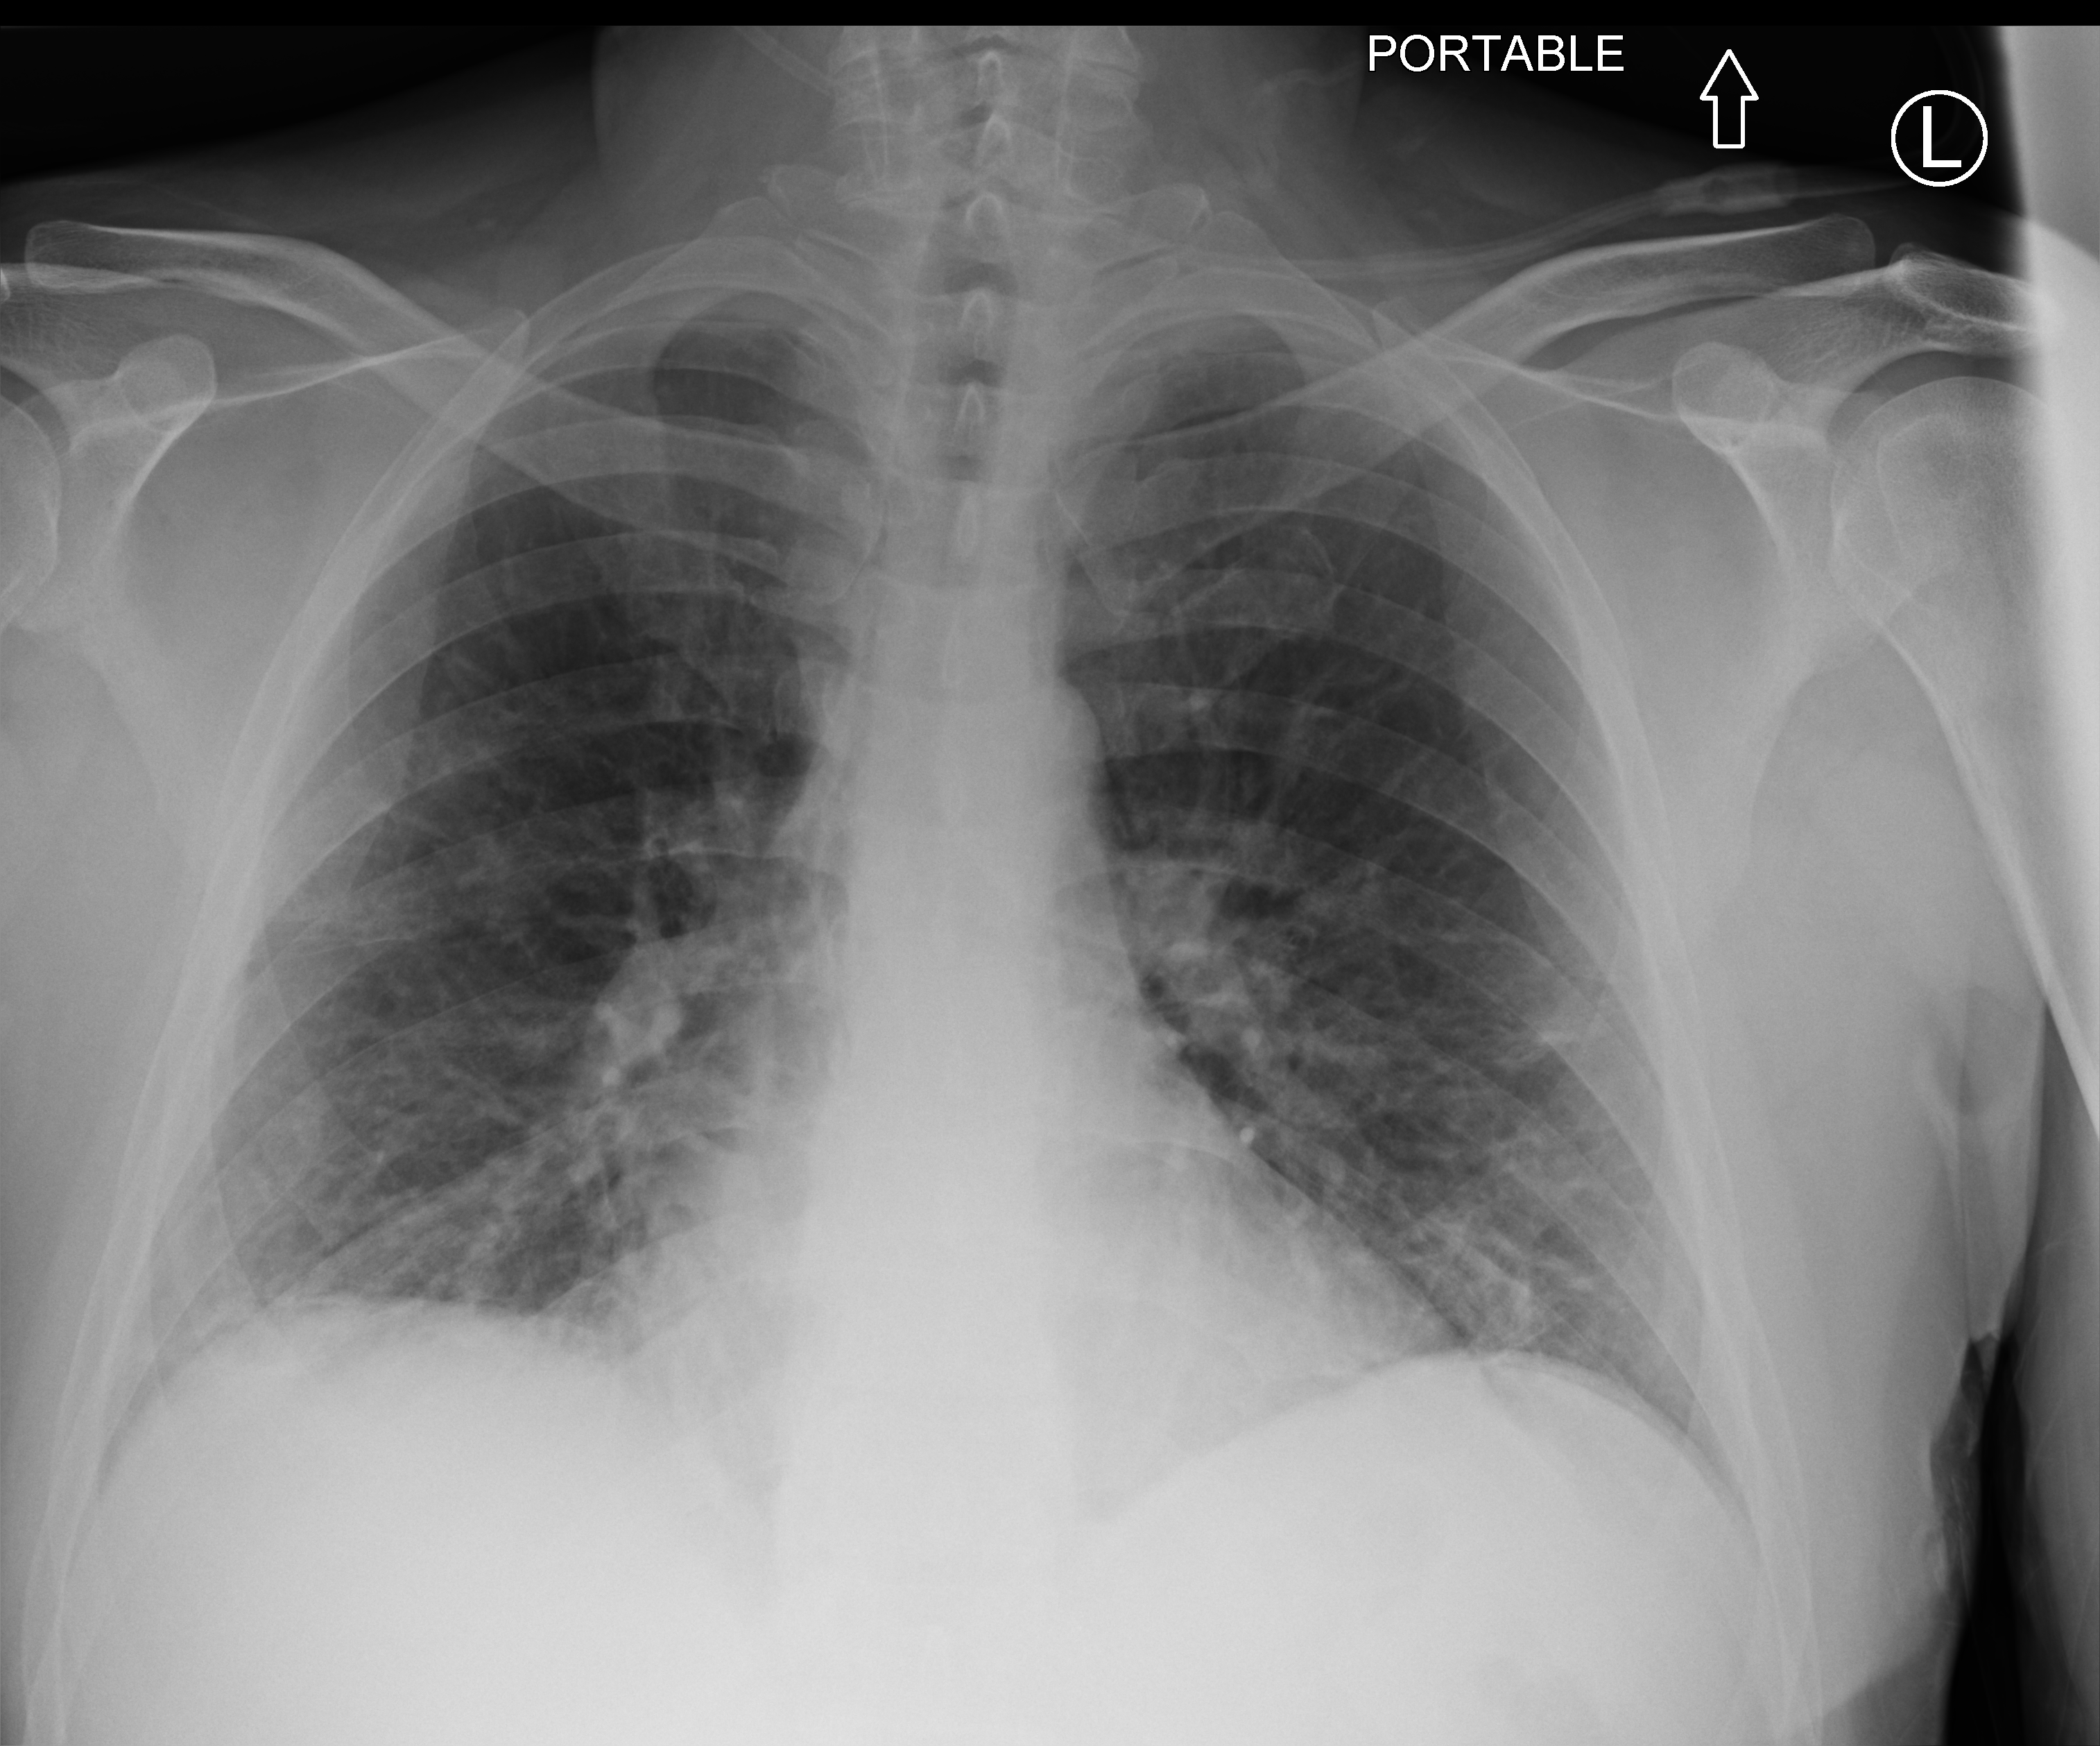
Portable chest radiograph. Male patient hospitalised with COVID-19, age 60–74 years.
Admission-level facts for this patient (not findings on this image; timing relative to this image not recorded):
- mechanically ventilated during this hospital stay: no
- length of hospital stay: 16 days